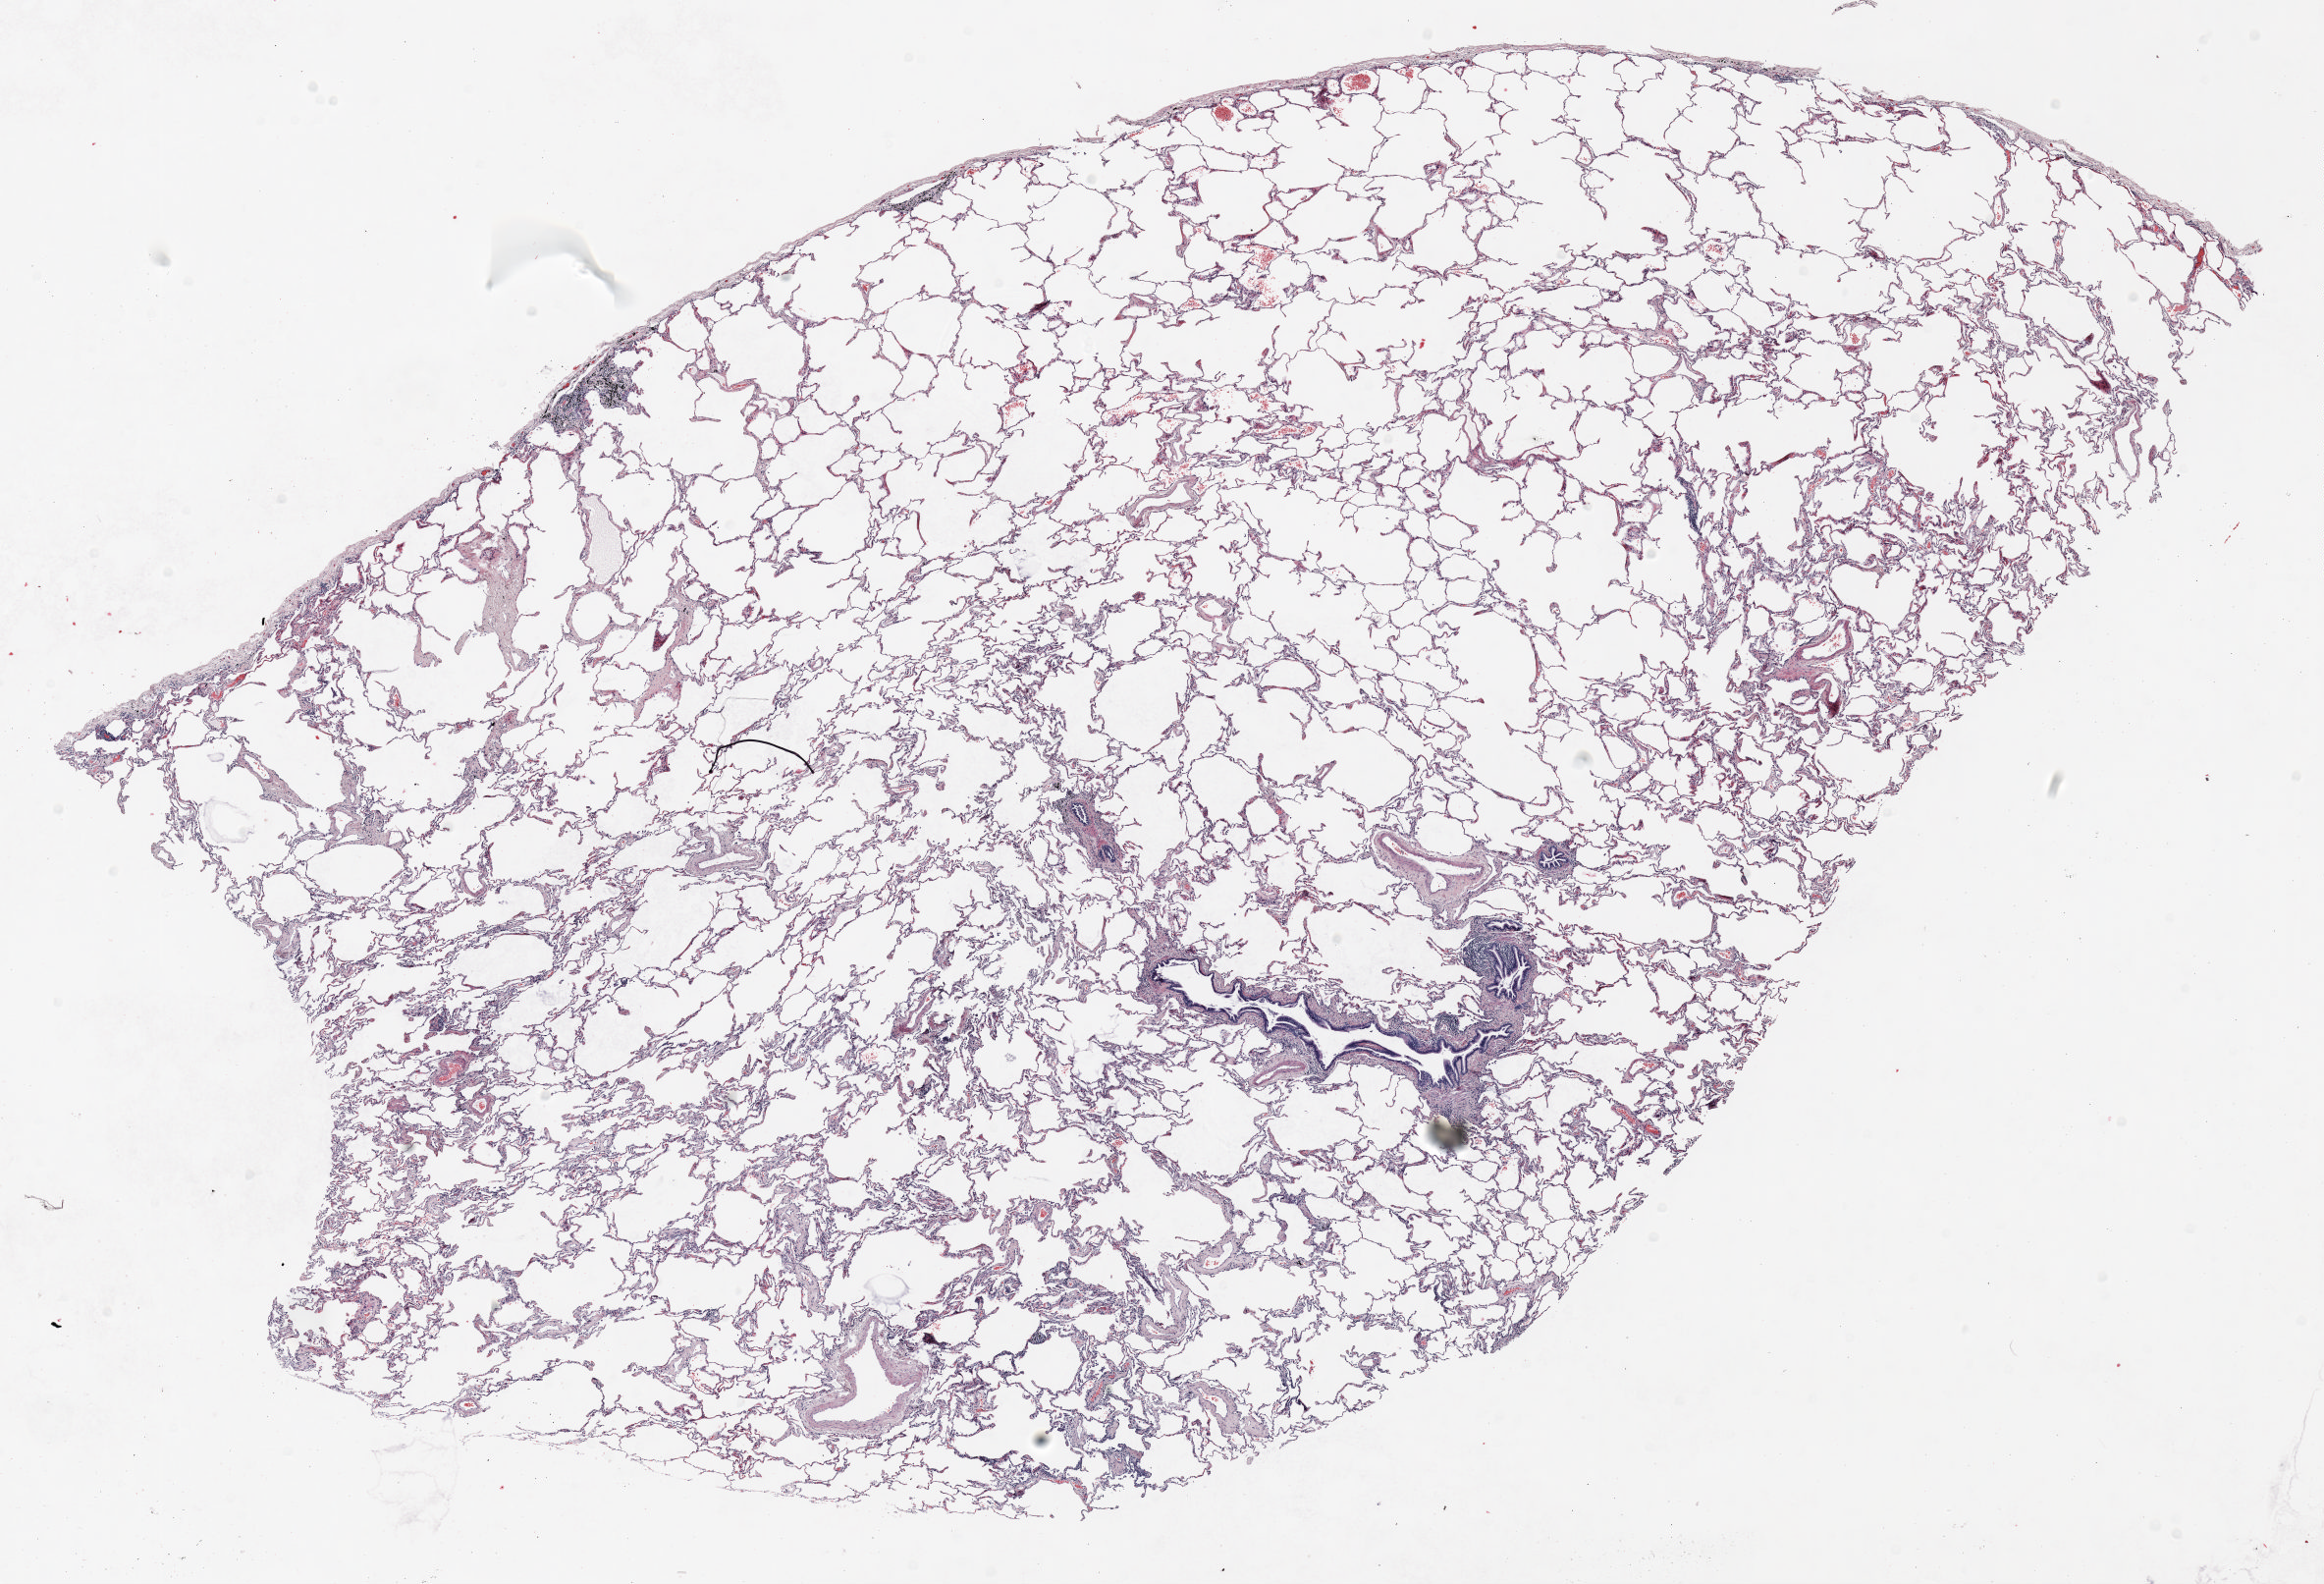
Whole-slide histology image, H&E-stained, whole scanned area (about 19.0 x 13.0 mm) shown as a low-resolution overview. Formalin-fixed paraffin-embedded (FFPE) section. Lung. Female, age 68 at enrolment. Grade: moderately differentiated (G2).
• primary tumour location (clinical record): right upper lobe
• tumour size (pathology): 31 mm
• stage (AJCC 6th edition): IB
• participant's lung-cancer diagnosis: Adenocarcinoma, NOS